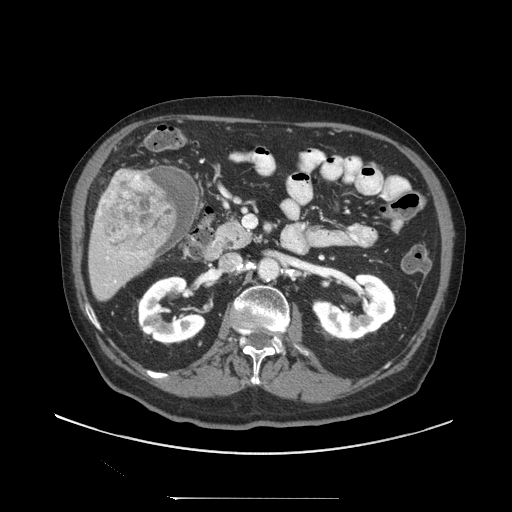
Contrast-enhanced abdominal CT (liver protocol), one axial slice; position 39 of 97 along the scan axis; 140 kVp; soft-tissue window (W 400 / L 40 HU); 2.5 mm slice thickness; 512 × 512 image matrix, field of view 450 × 450 mm. From the clinical record (not read from this slice): diagnosis: hepatocellular carcinoma (patient treated with transarterial chemoembolisation; whether this scan precedes or follows treatment is not stated here); TNM stage (as recorded): Stage-IIIC; Child-Pugh class: A; tumour nodularity: uninodular.
Structures marked on this image (semi-automatically segmented with operator editing):
- liver parenchyma outside the tumour (the mass and vessels are separate outlines, so this box may not span the whole liver): bounding box <88,166,198,300> (left, top, right, bottom; pixels)
- mass: <101,172,177,253>
- liver vessels: <98,200,116,282>